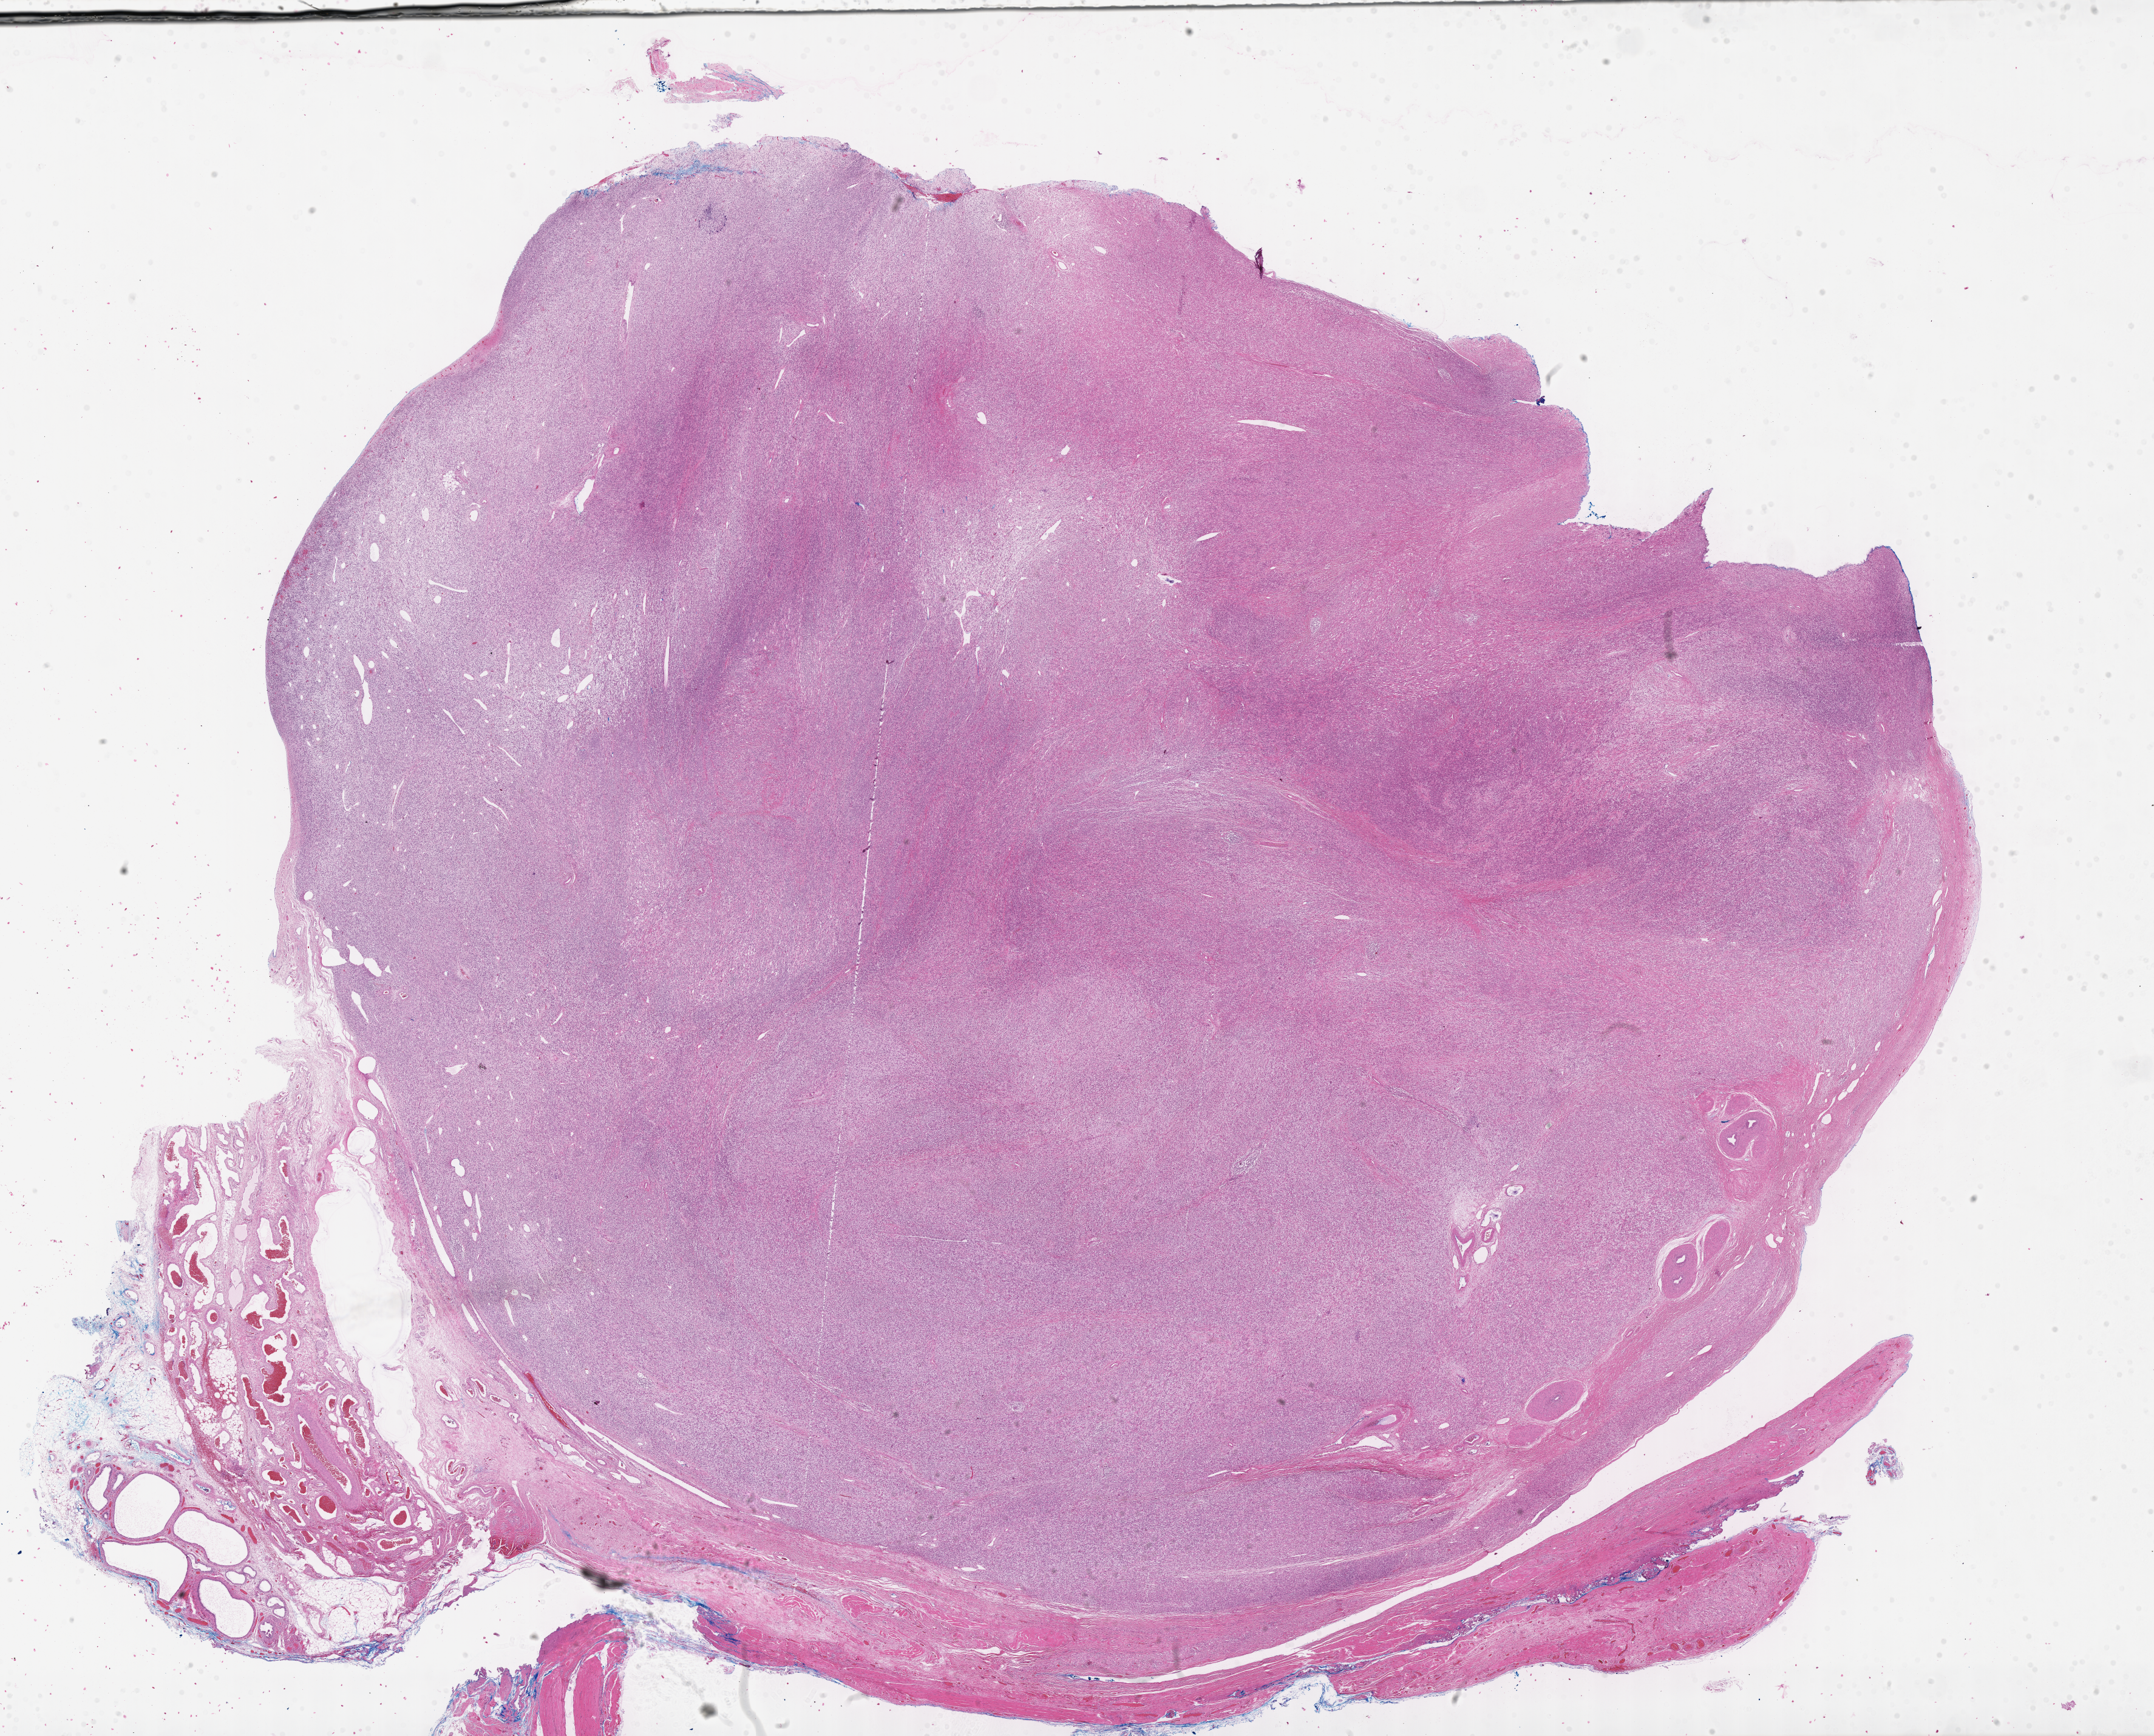
Digitized H&E-stained section of tumor tissue, a low-resolution overview of the entire scanned area, about 28.7 x 23.1 mm; formalin-fixed, paraffin-embedded (FFPE) tissue; sample anatomic site: testicle-right. Male patient, age at diagnosis 0.9 years.
* diagnosis: rhabdomyosarcoma; histological classification: embryonal rhabdomyosarcoma
* primary site (case record): testis-Paratestis
* stage (as recorded): 1